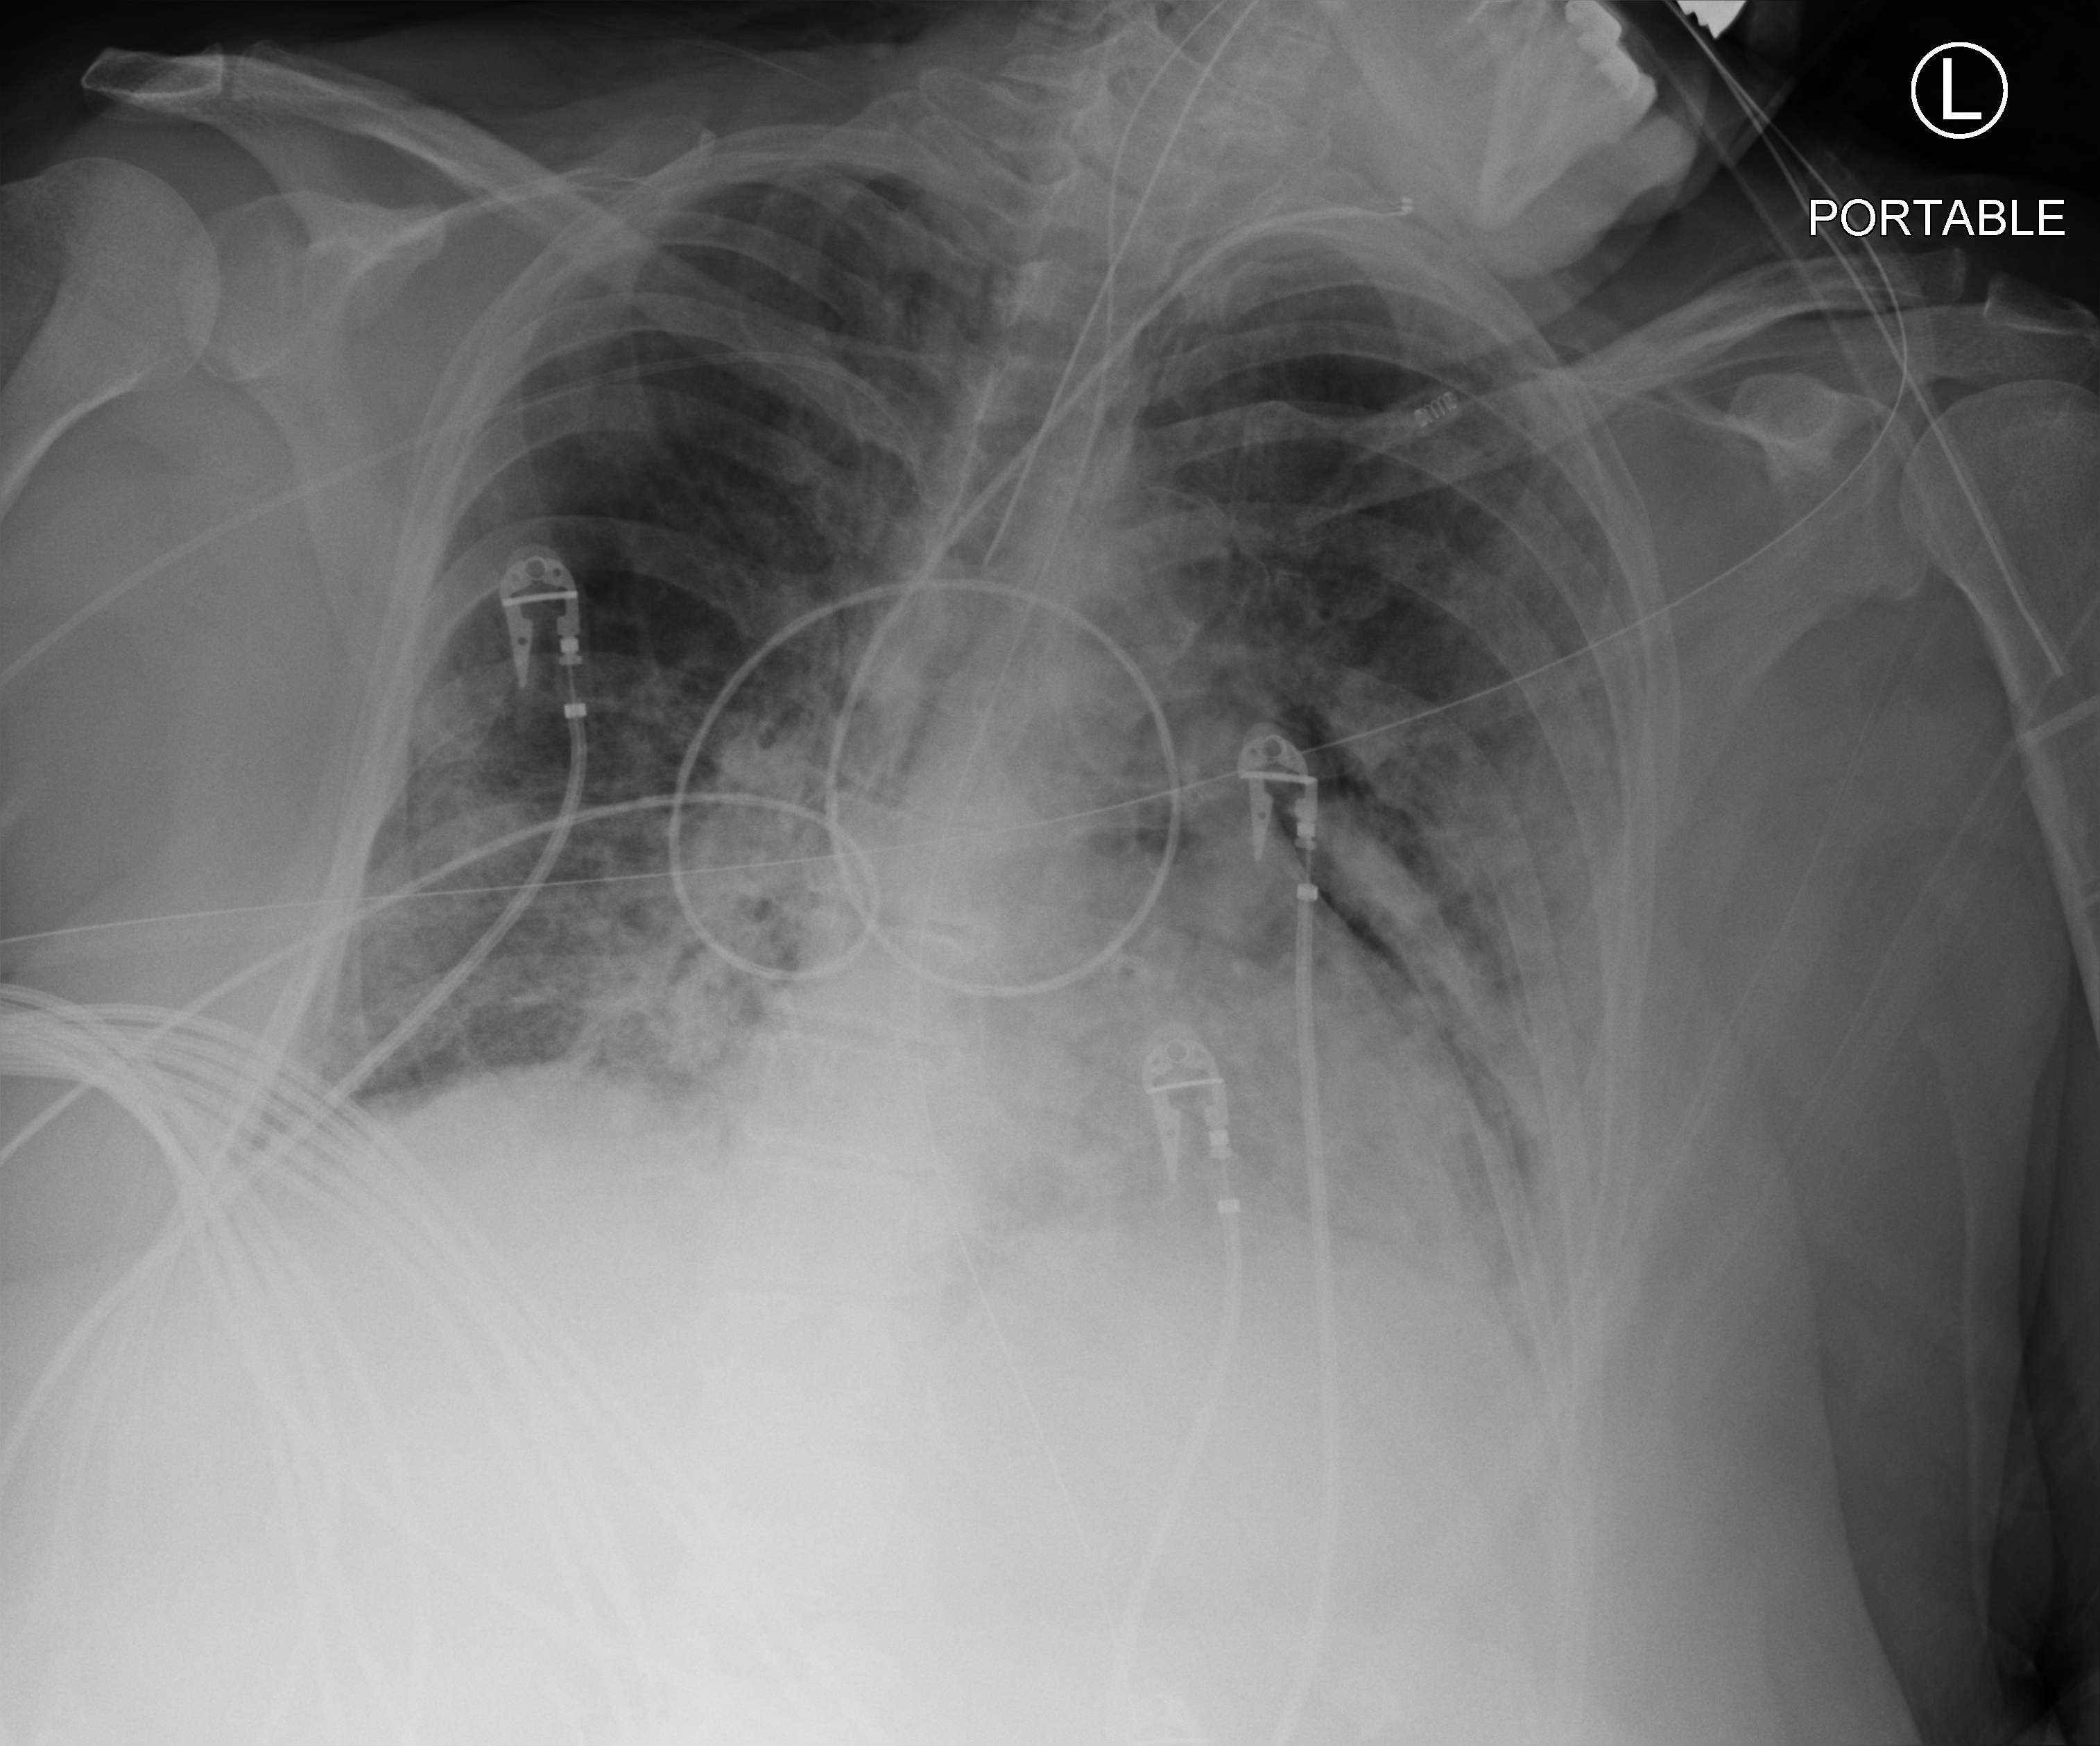
Bedside chest radiograph (computed radiography), anteroposterior (AP) projection. Female patient hospitalised with COVID-19, age 60–74 years.
From the hospital-stay record, not from the radiograph (when in the stay this image was taken is not recorded): admitted to intensive care during this hospital stay: yes; mechanically ventilated during this hospital stay: yes; diabetes (admission record): no.